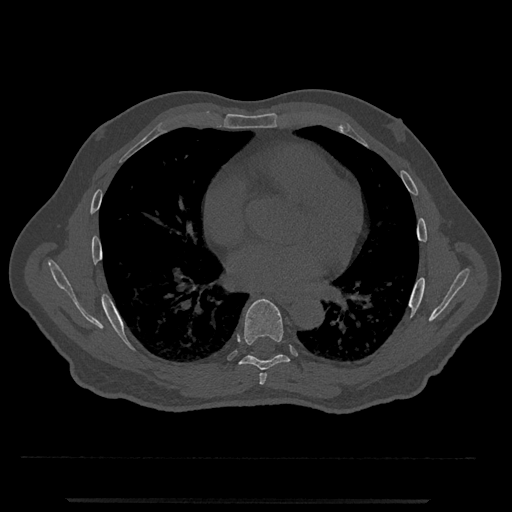
CT including the spine, one axial slice. Slice 680 of 797 in the series (ordered by position). Reconstruction kernel Br40s/3. 120 kVp. Bone window (W 1800 / L 400 HU). 0.5 mm slice thickness. 512 × 512 image matrix. Male patient, age 63 years. From the clinical record (not read from this slice): primary cancer: prostate.
Structures marked on this image (semi-automatically segmented with operator editing):
- T6 vertebra: bounding box (x1, y1, x2, y2) in pixels: (259, 373, 267, 385)
- T7 vertebra: (235, 299, 290, 370)